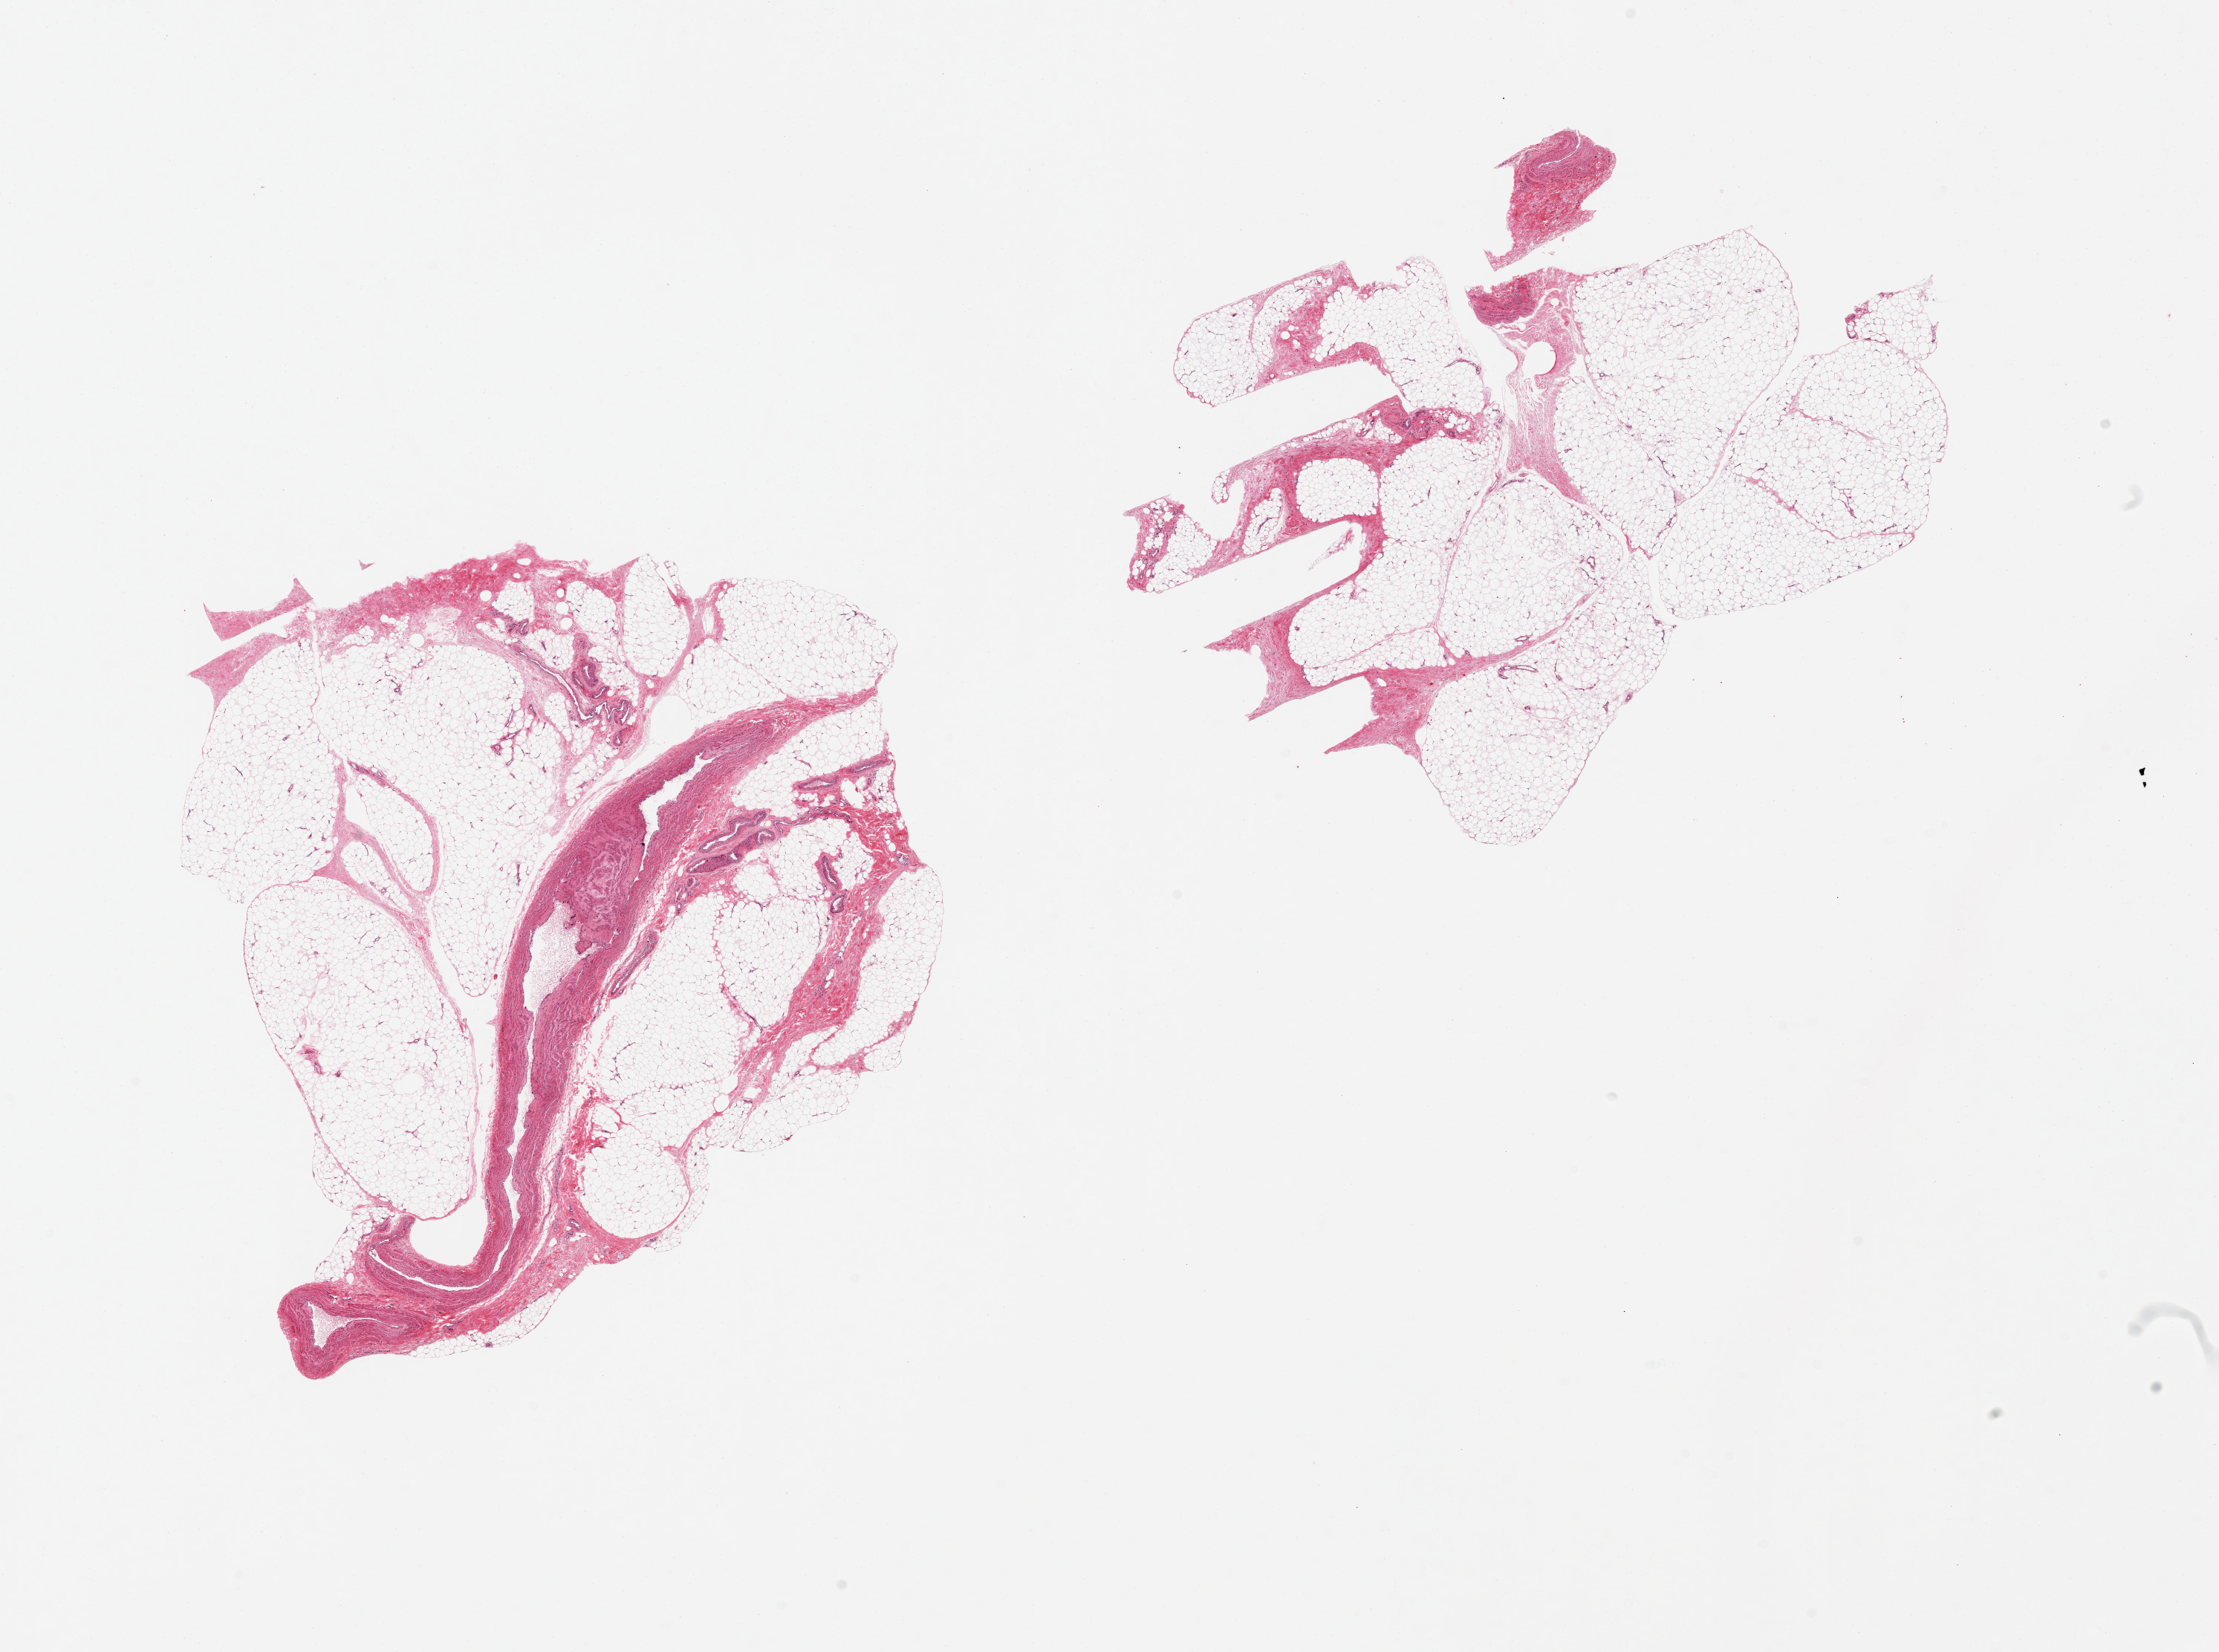
Digitized haematoxylin and eosin-stained section, brightfield, a low-resolution overview of the entire scanned area, about 23.6 x 17.6 mm; PAXgene-fixed, paraffin-embedded tissue; sampled site (target tissue): adipose tissue; donor tissue sample. Donor sex: male.
Reviewer comment on this tissue sample: 2 pieces; large vein =10% of 1 piece.